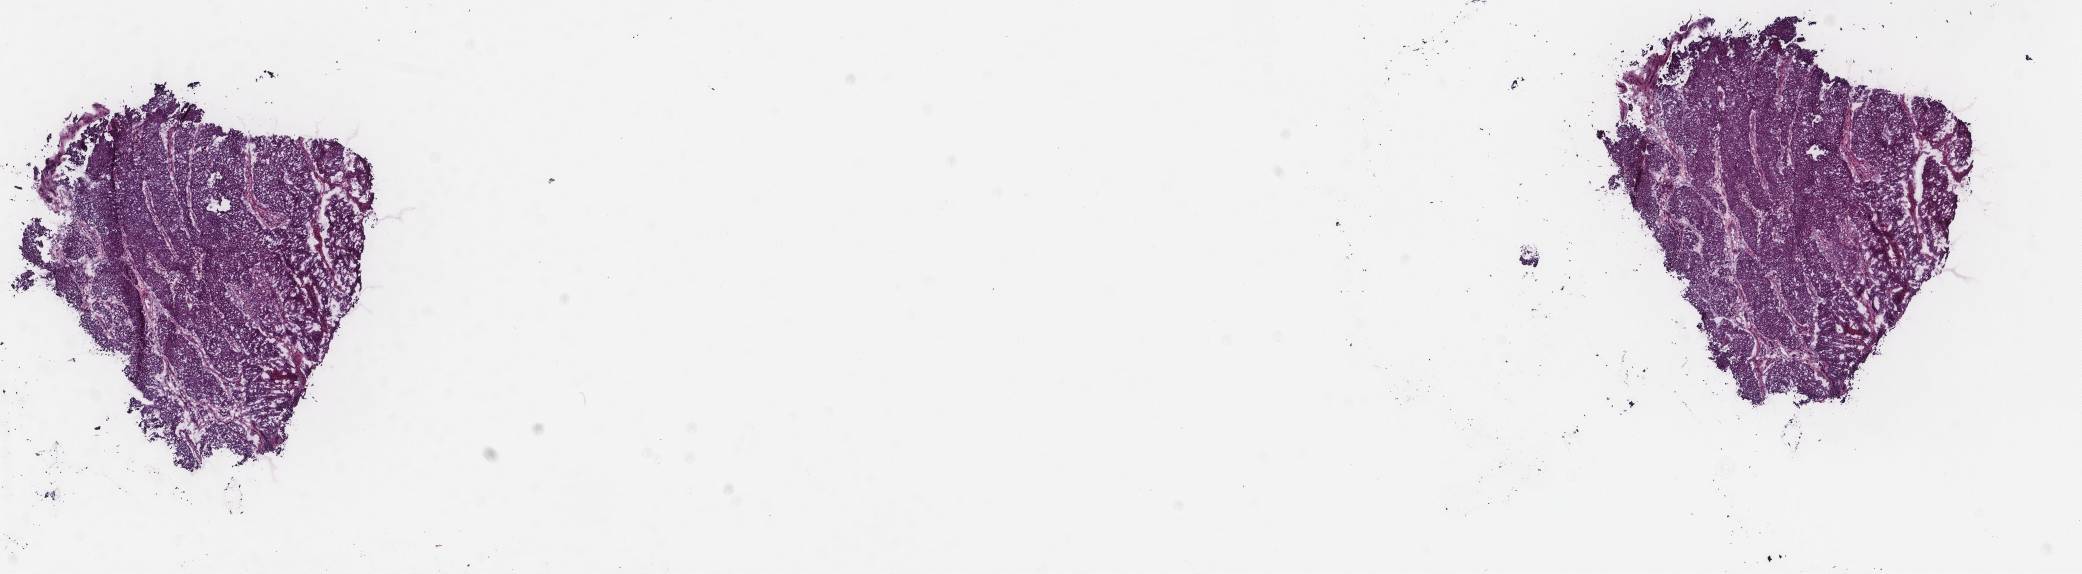
Whole-slide histology image, Hematoxylin and eosin (H&E) stained, shown as a low-resolution overview of the whole scanned area (about 16.5 x 4.6 mm, slide scanned at 40x). Frozen section from the top of the tissue portion. Bladder, primary tumour sample. Patient: male, age at initial diagnosis 85 years. Histologic grade: high grade. Composition of this section per pathologist review: tumour cells 78%, tumour nuclei 90%, normal cells 0%, stromal cells 17%, necrosis 5%. Infiltration values recorded for this section: lymphocyte infiltration 2%, monocyte infiltration 1%, neutrophil infiltration 0%.
AJCC pathologic stage: IV (6th edition). Pathologic diagnosis: Transitional cell carcinoma (lateral wall of bladder). Lymph nodes positive (case pathology): 2 of 18 examined.